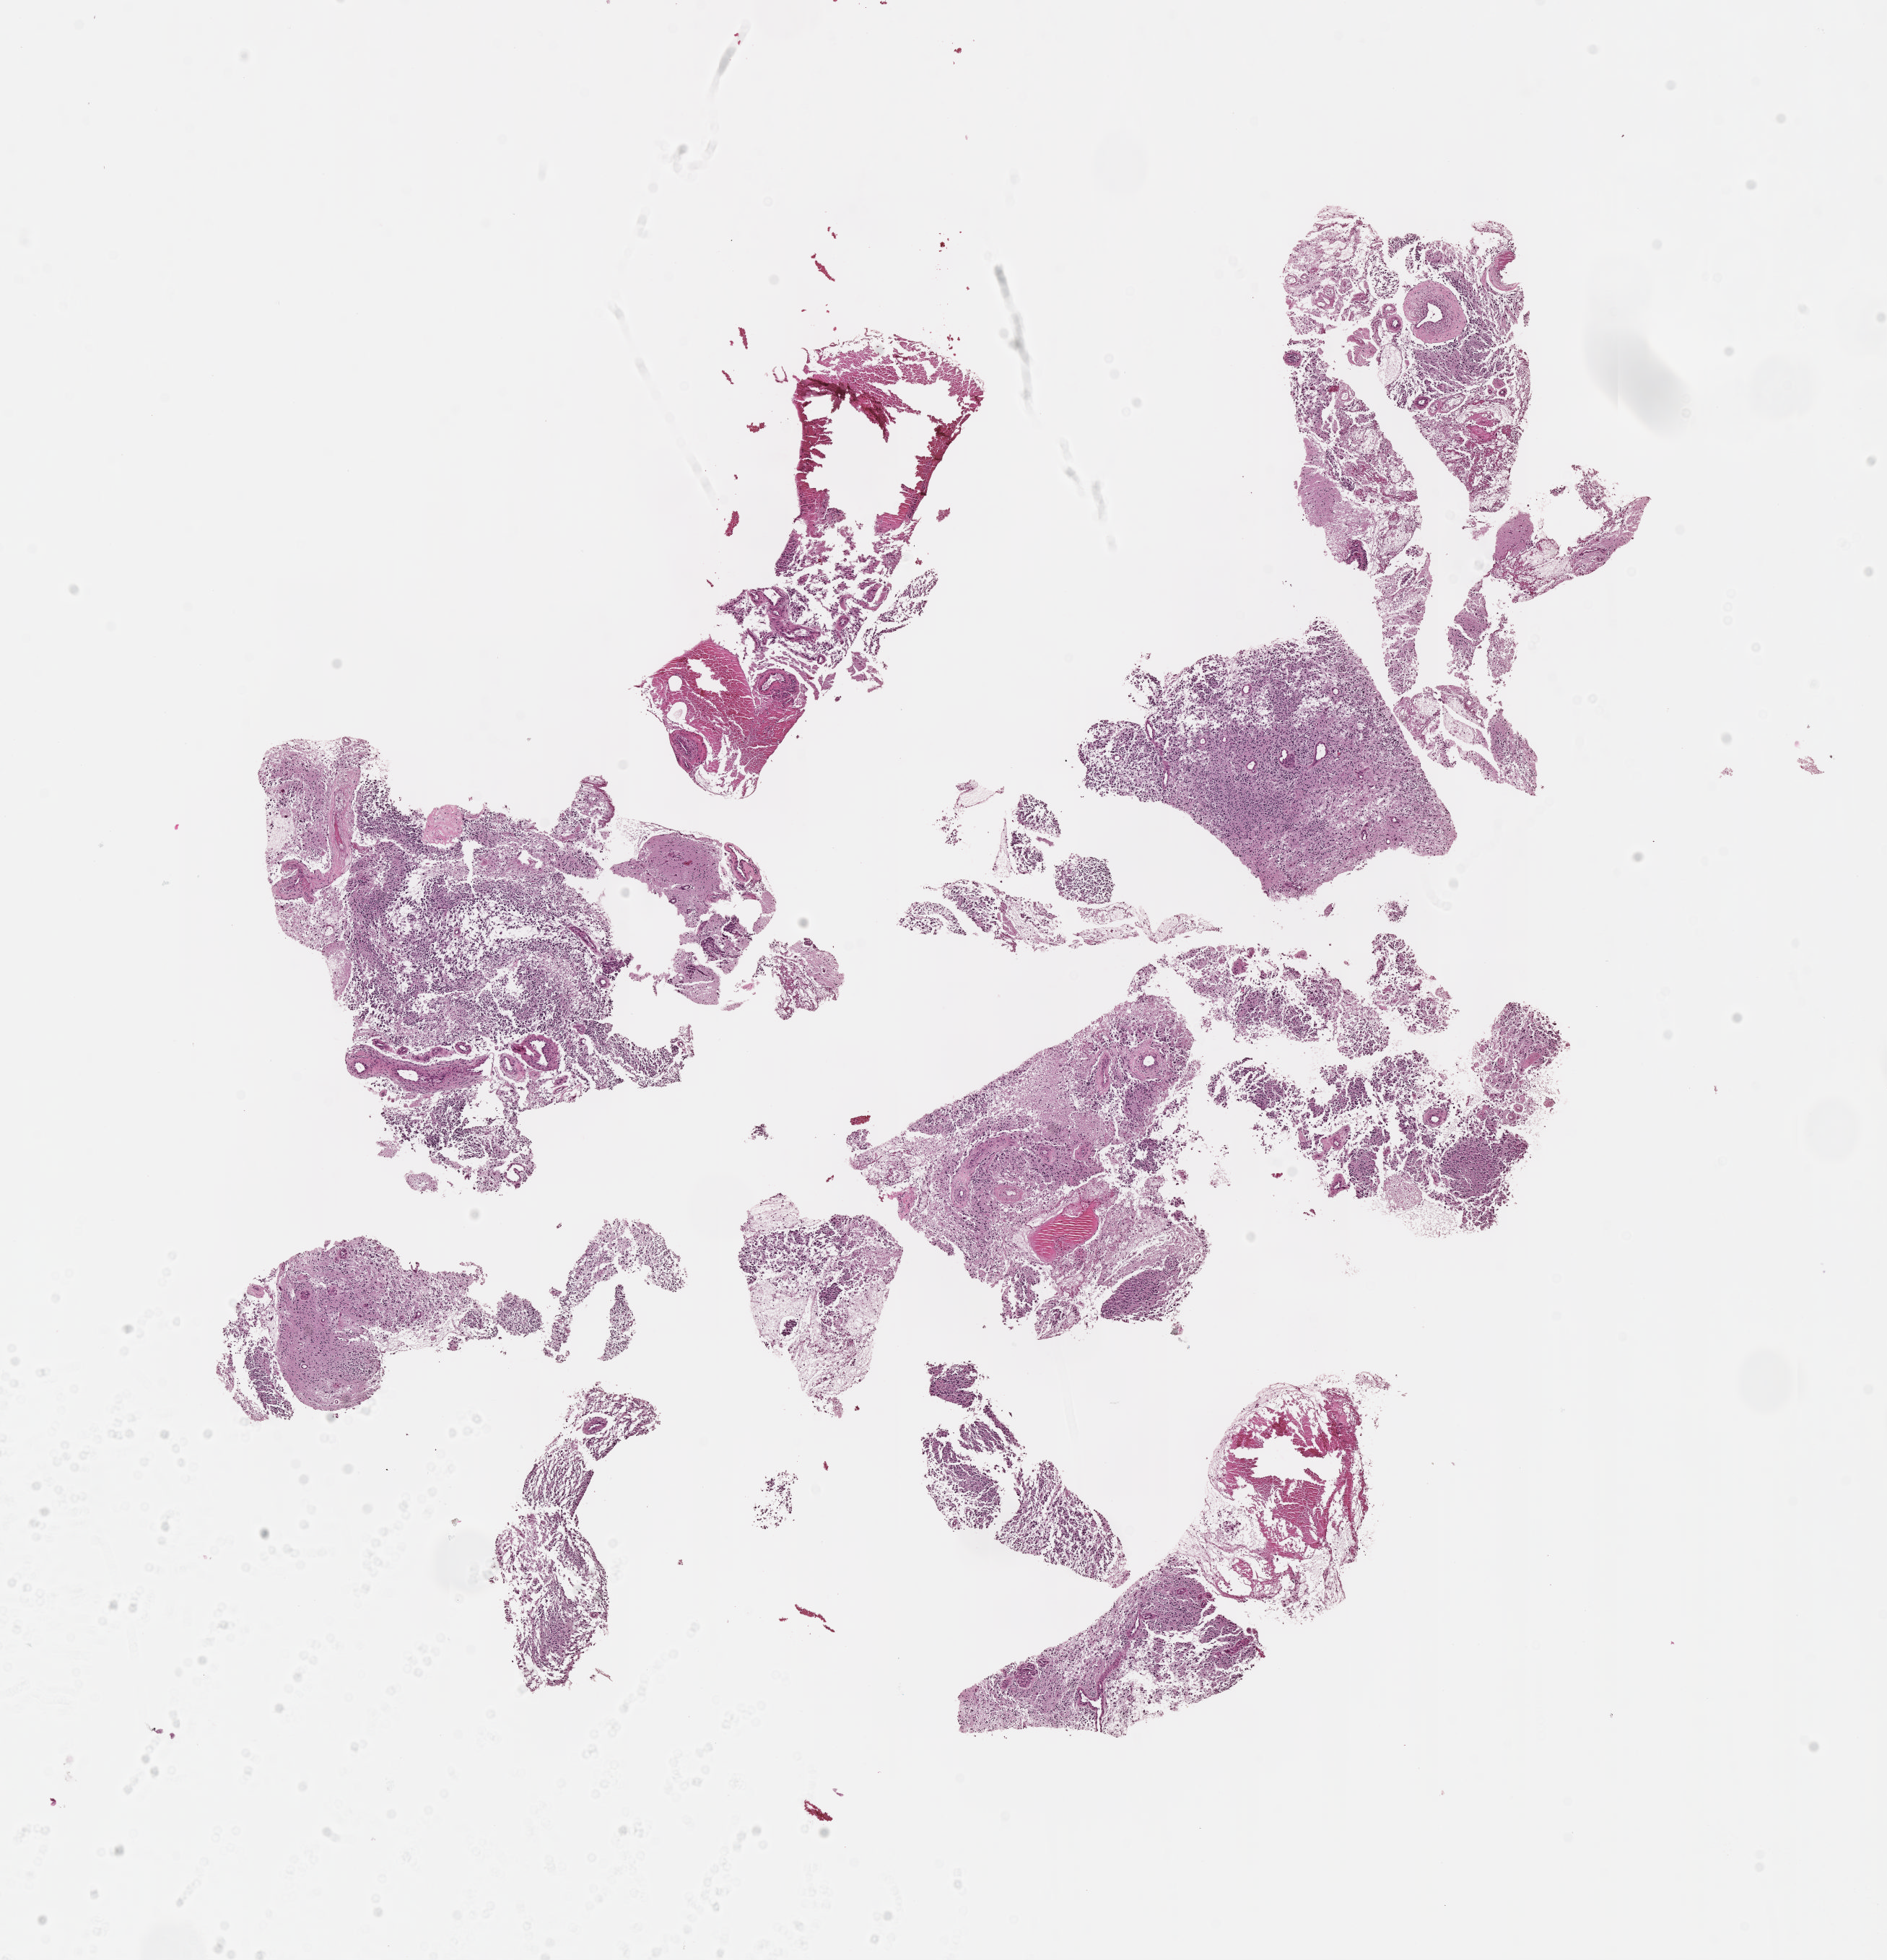
Whole-slide histology image, Hematoxylin and eosin (H&E) stained, whole scanned area (about 10.6 x 11.0 mm) shown as a low-resolution overview; formalin-fixed paraffin-embedded (FFPE) diagnostic section; sample: primary tumour, brain. Male, age 54 years at initial diagnosis.
Diagnosis: Oligodendroglioma, anaplastic.